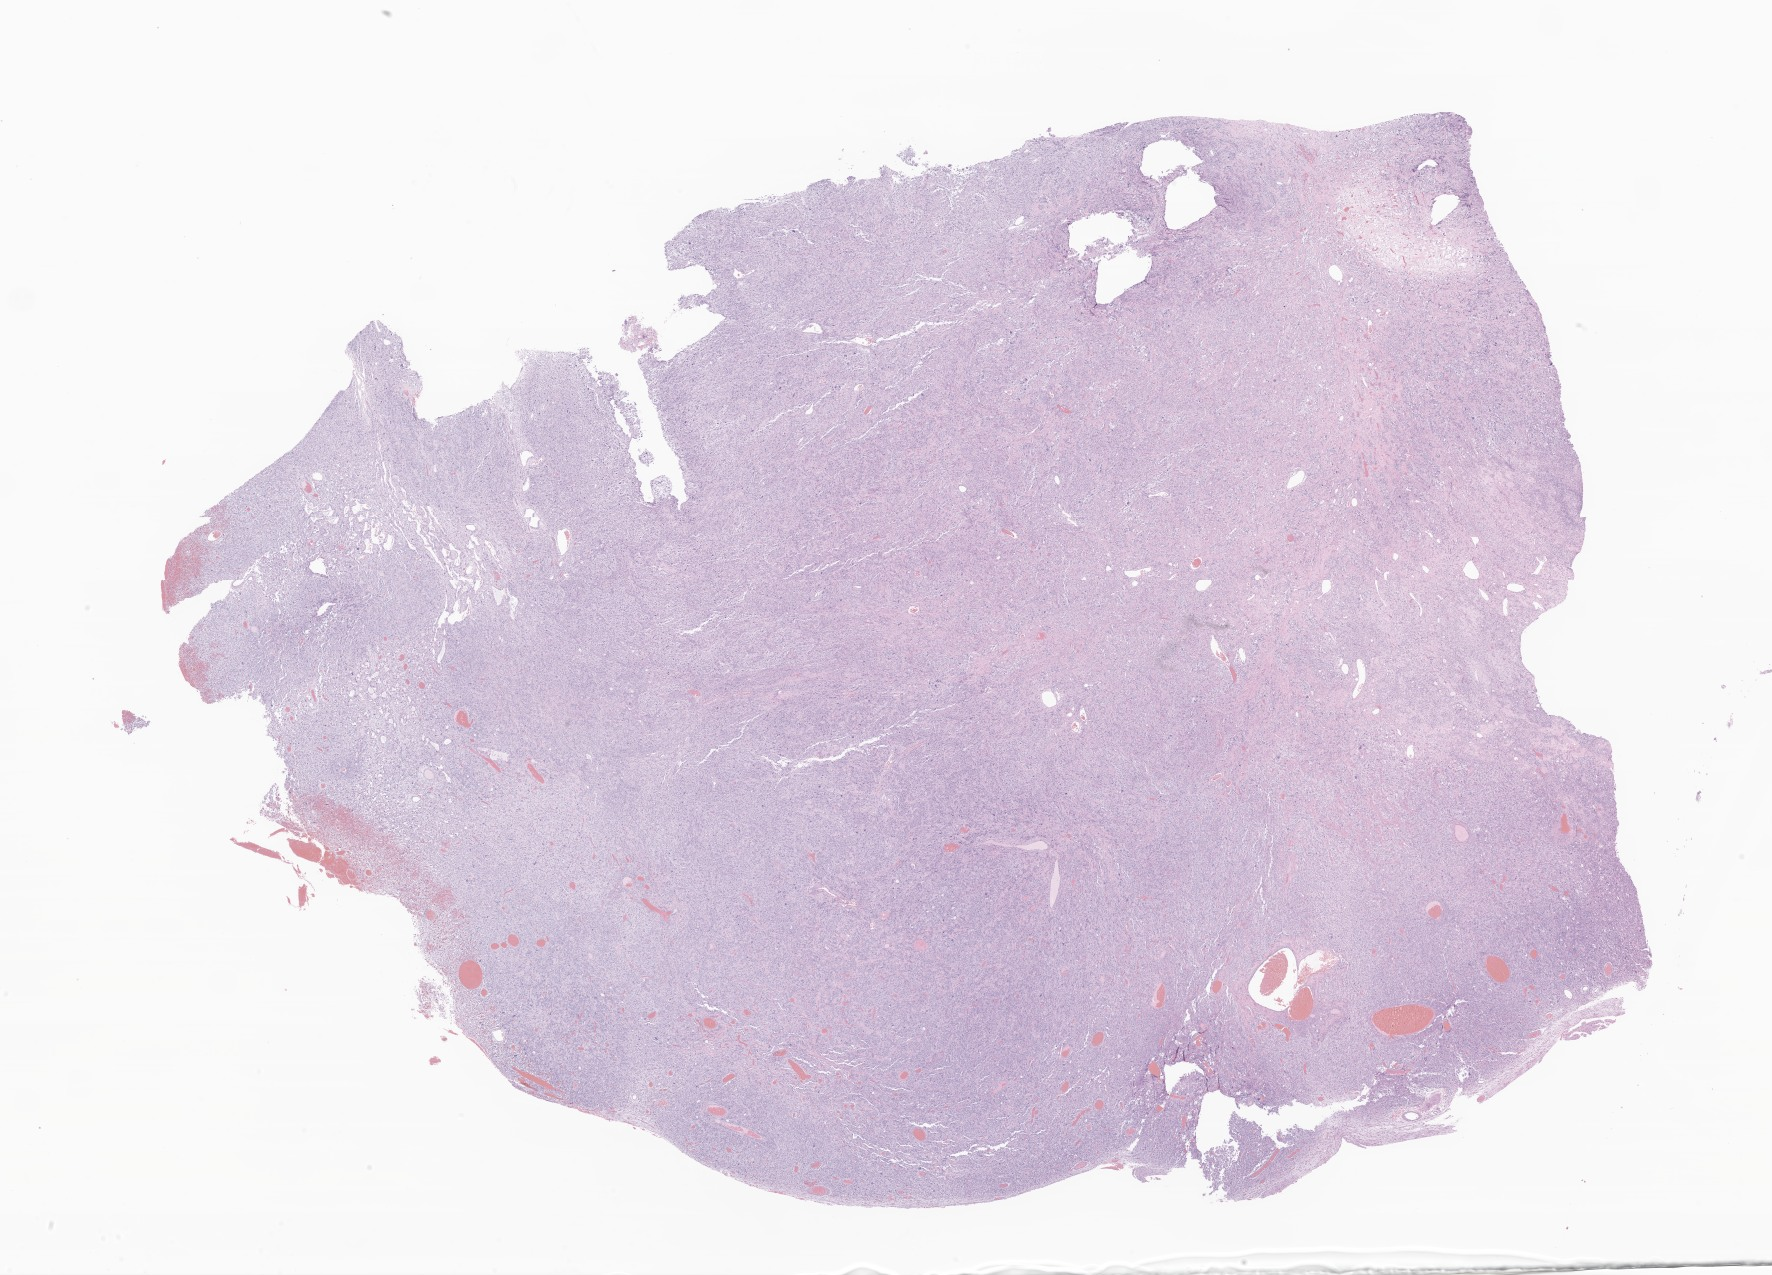
Digitized haematoxylin and eosin-stained section of tumor tissue from the parietal lobe — a low-resolution overview of the entire scanned area, about 29.9 x 21.5 mm; FFPE section. Male patient, age 76 months (6 years 4 months).
Recorded diagnosis: Neoplasm, uncertain whether benign or malignant.